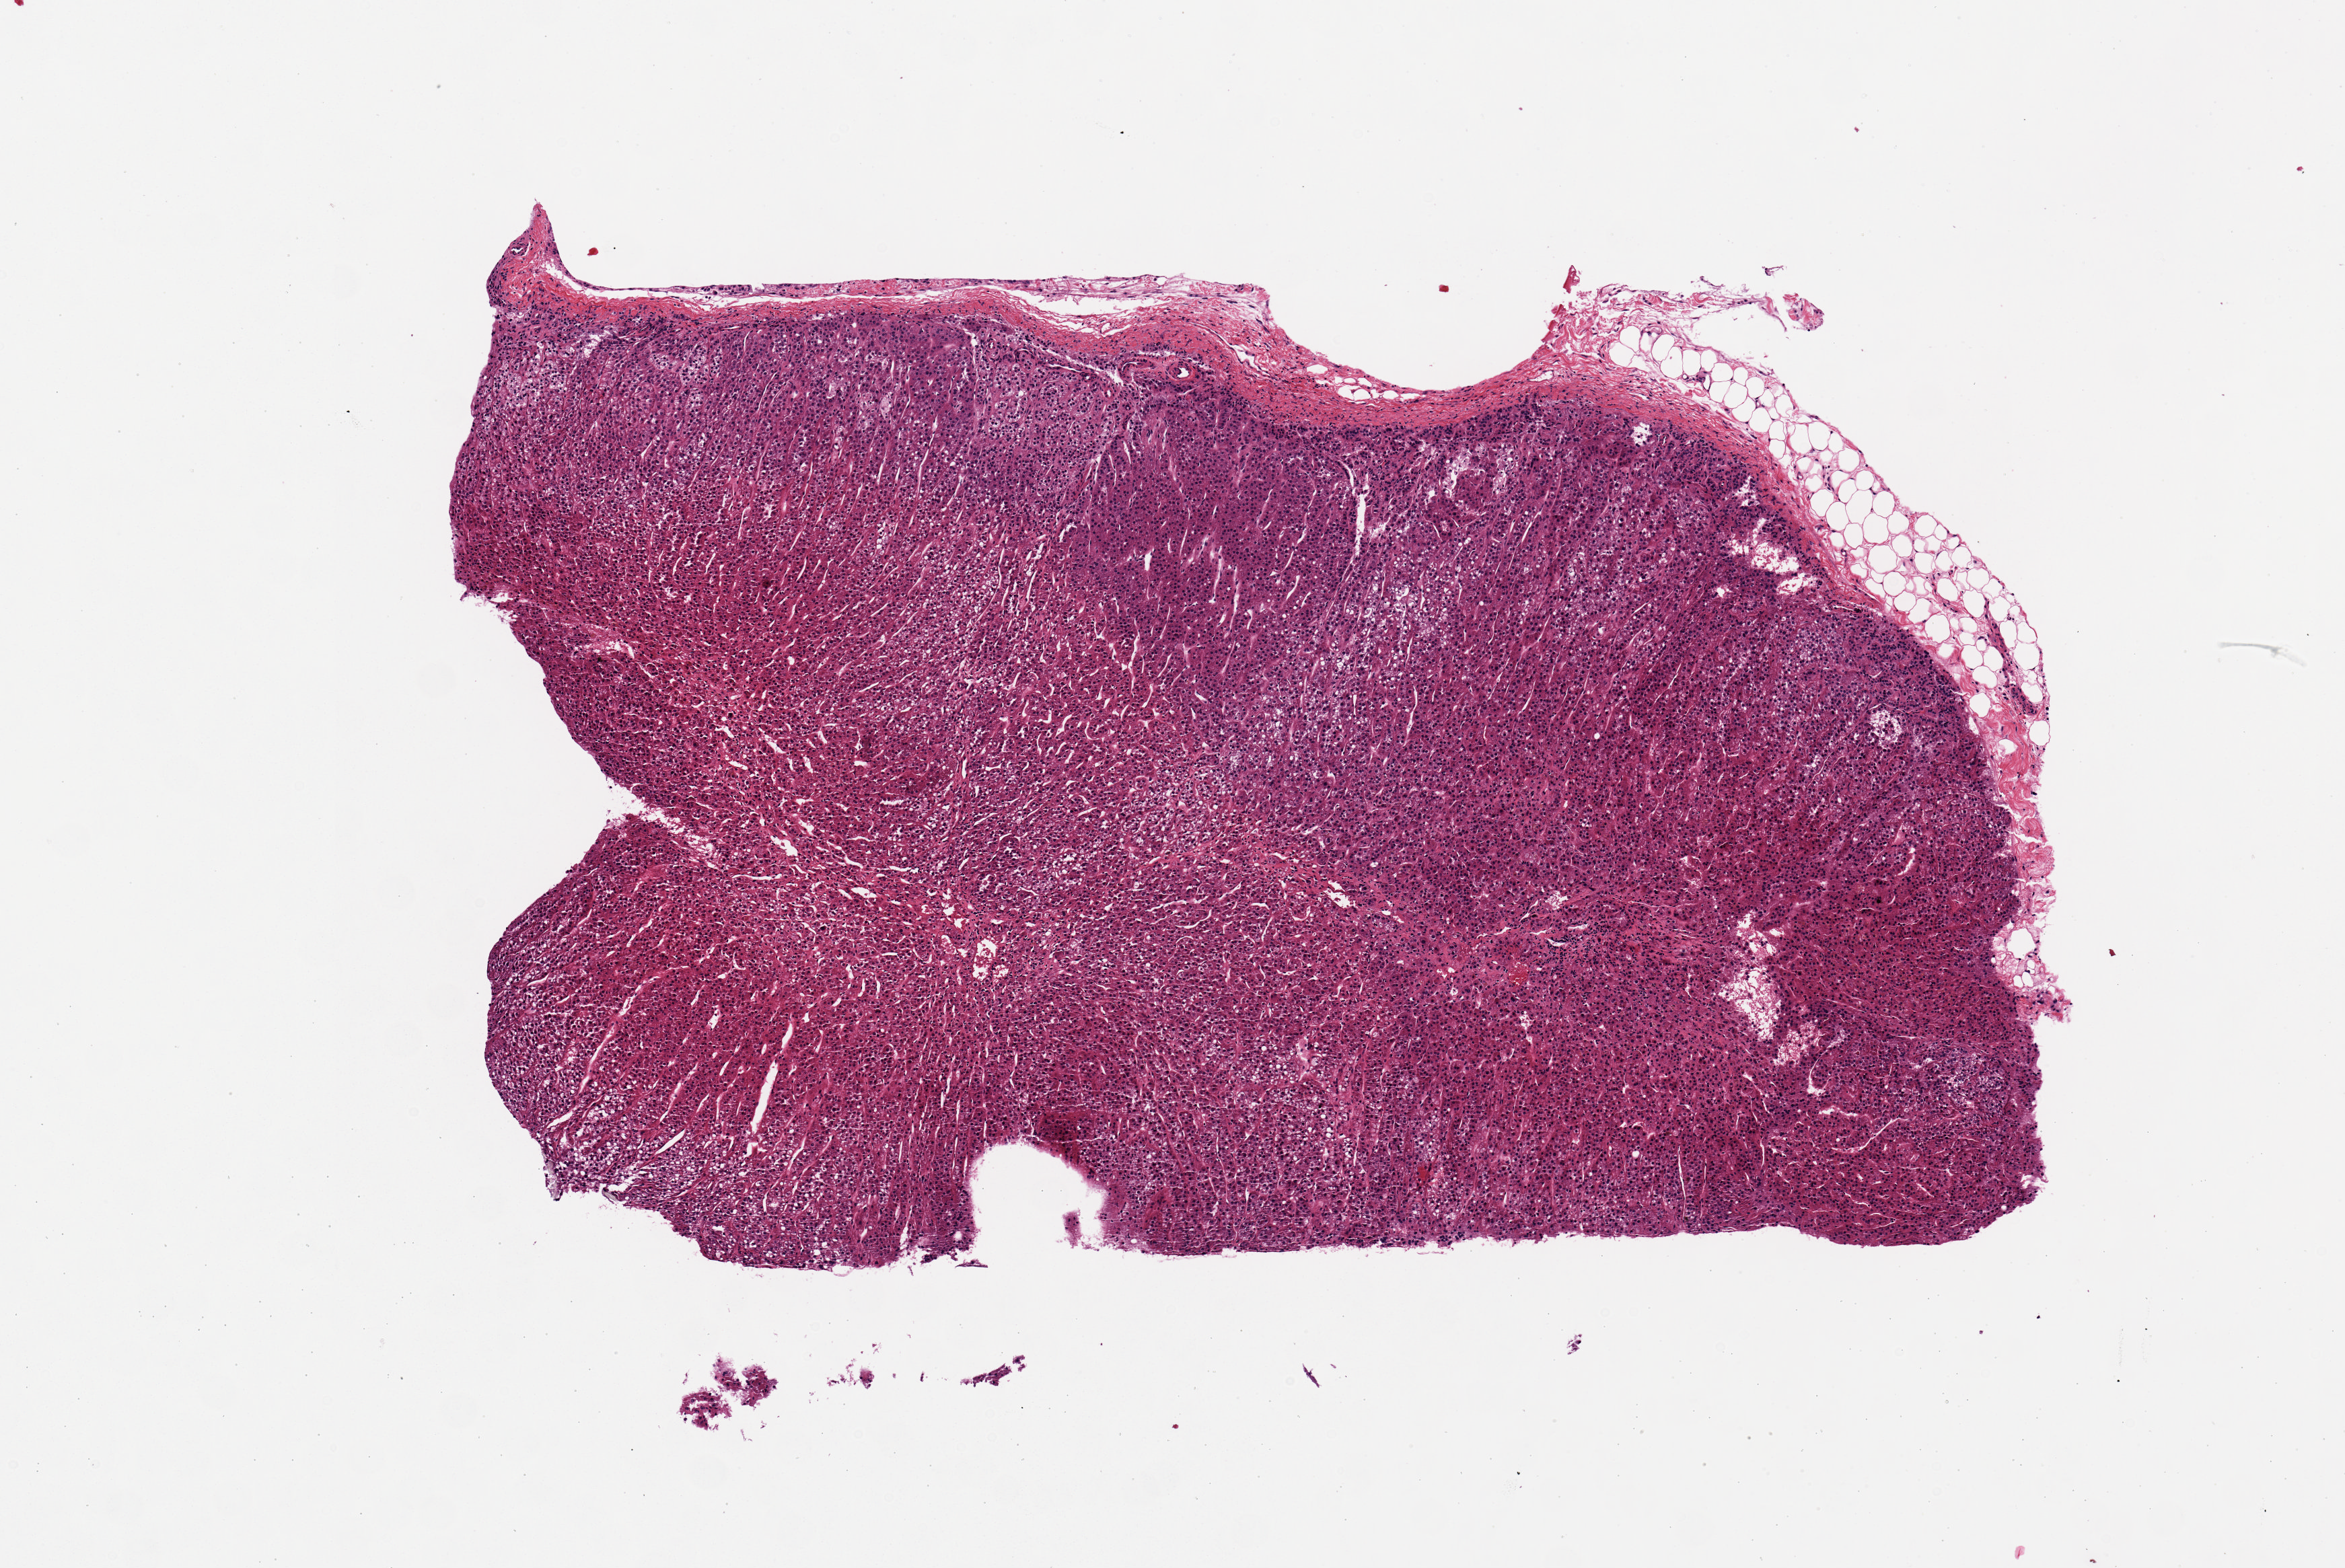
Whole-slide image, haematoxylin and eosin stain, brightfield, whole scanned area (about 6.9 x 4.6 mm, acquisition: 20x scan) shown as a low-resolution overview. PAXgene-fixed, paraffin-embedded tissue. Target tissue: adrenal gland. Tissue donor sample.
* review note (as recorded): Well preserved cortex